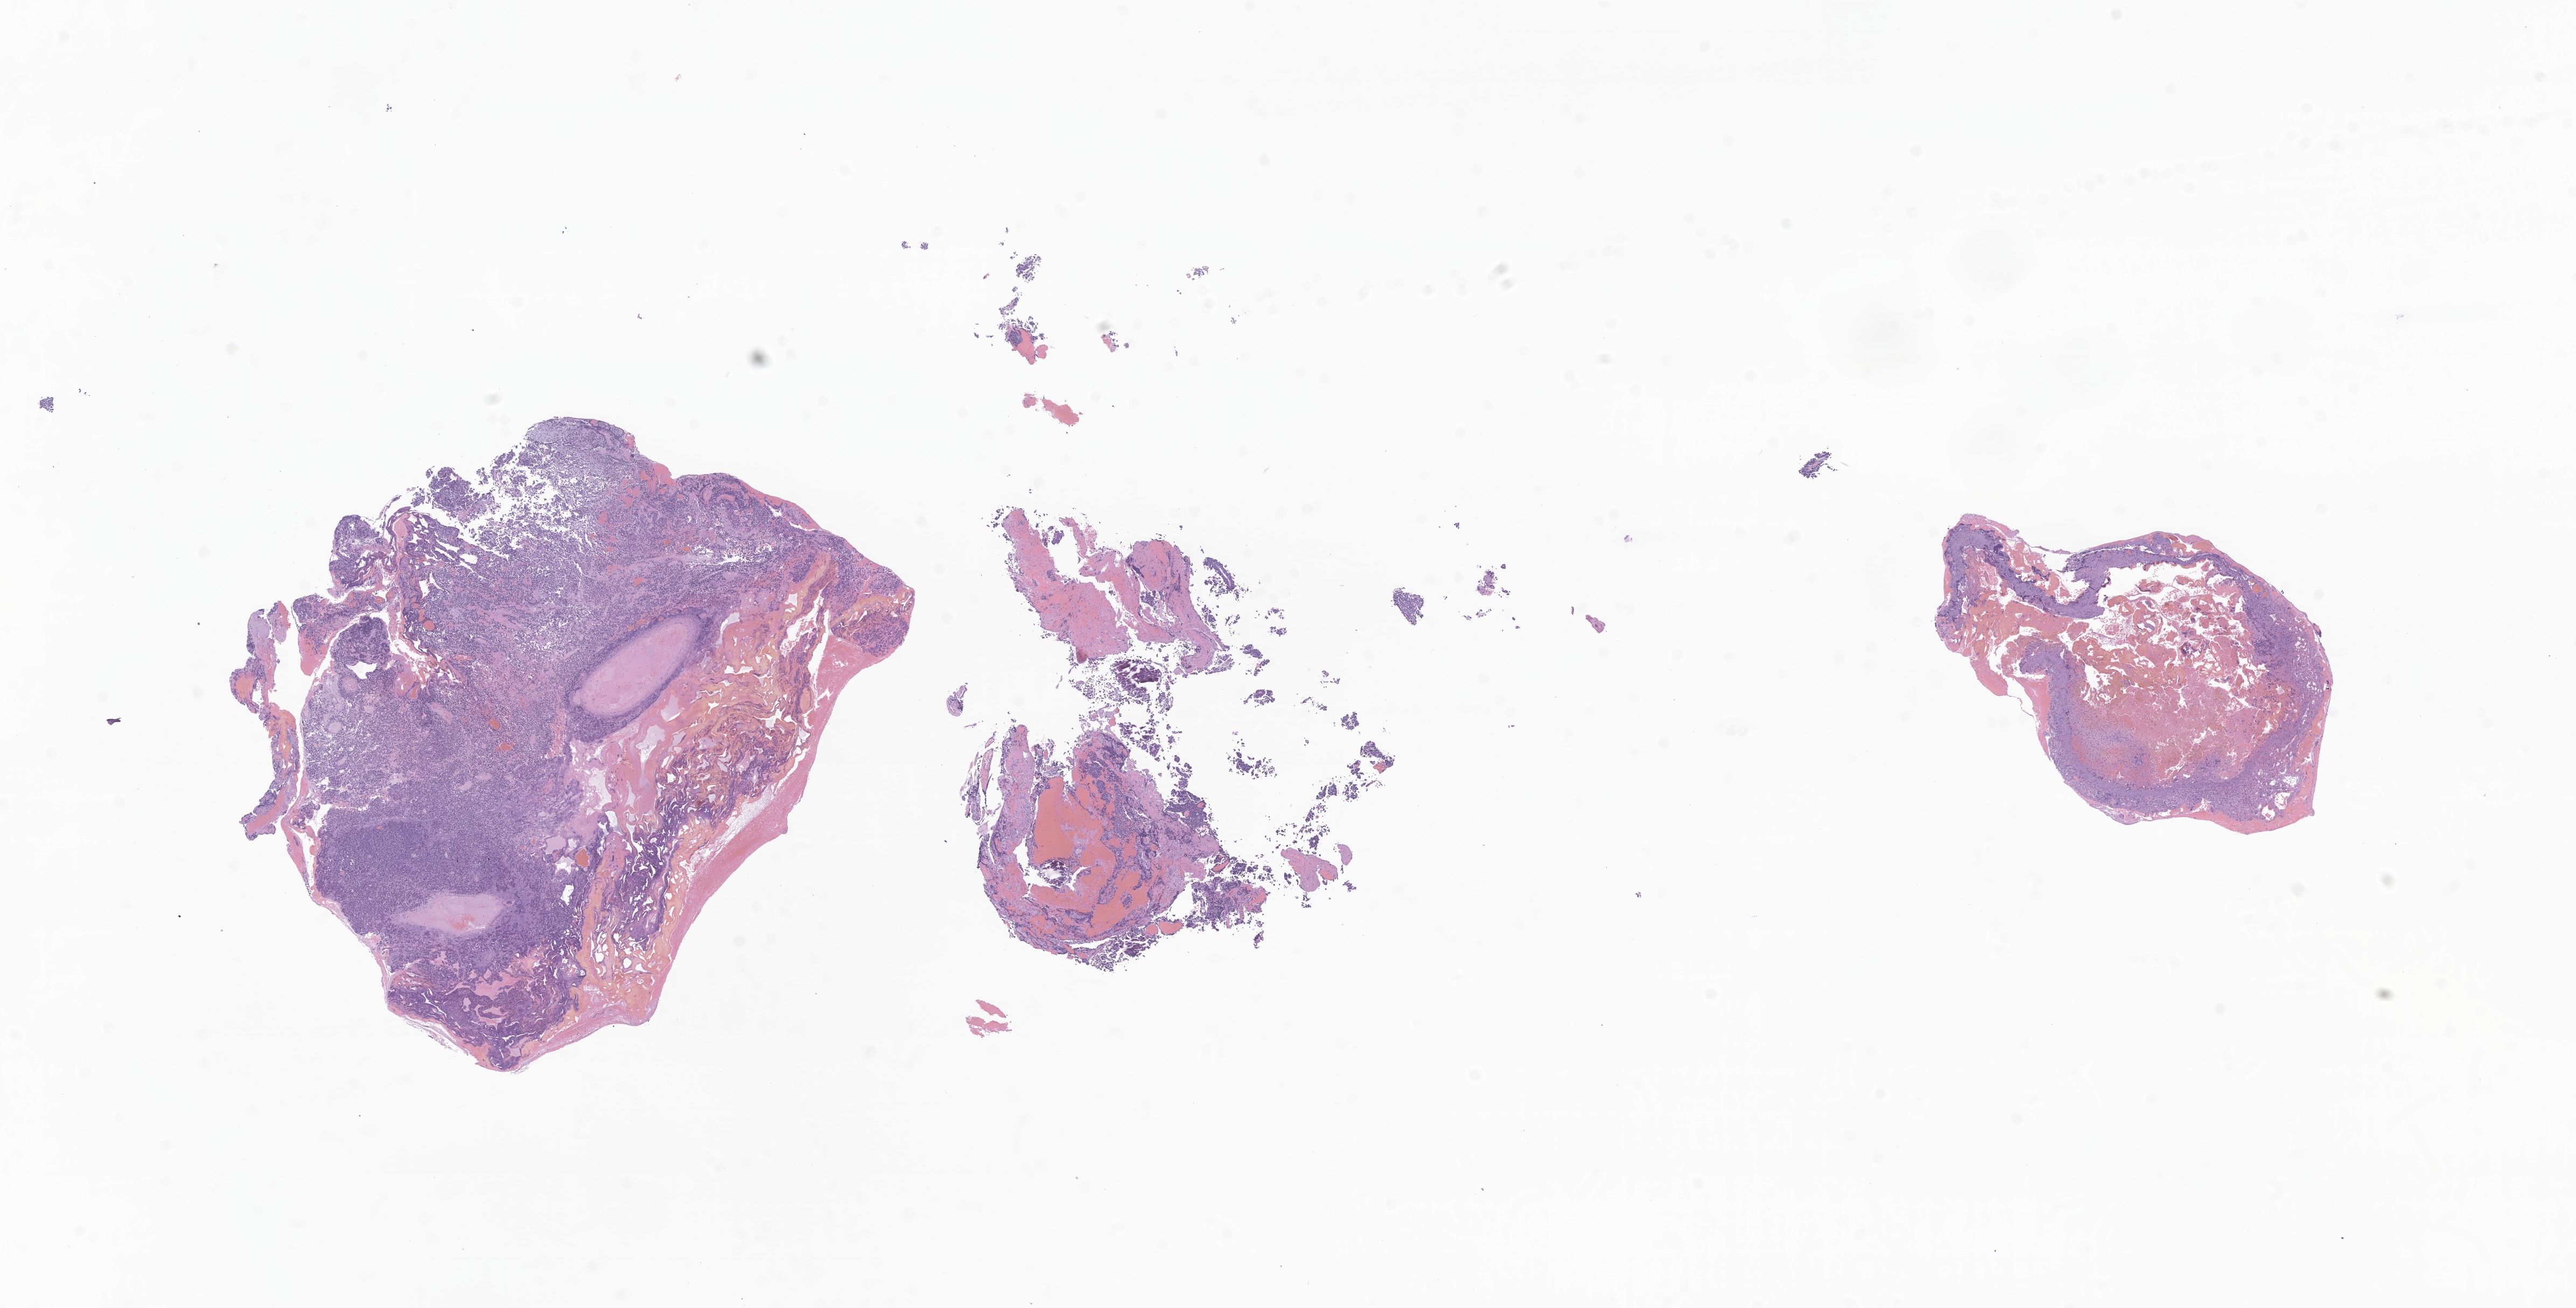
H&E whole-slide image of tumor tissue from the brain — shown as a low-resolution overview of the whole scanned area (about 20.2 x 10.2 mm); formalin-fixed, paraffin-embedded (FFPE) tissue. Patient female; age 105 months.
- recorded diagnosis: Pineoblastoma